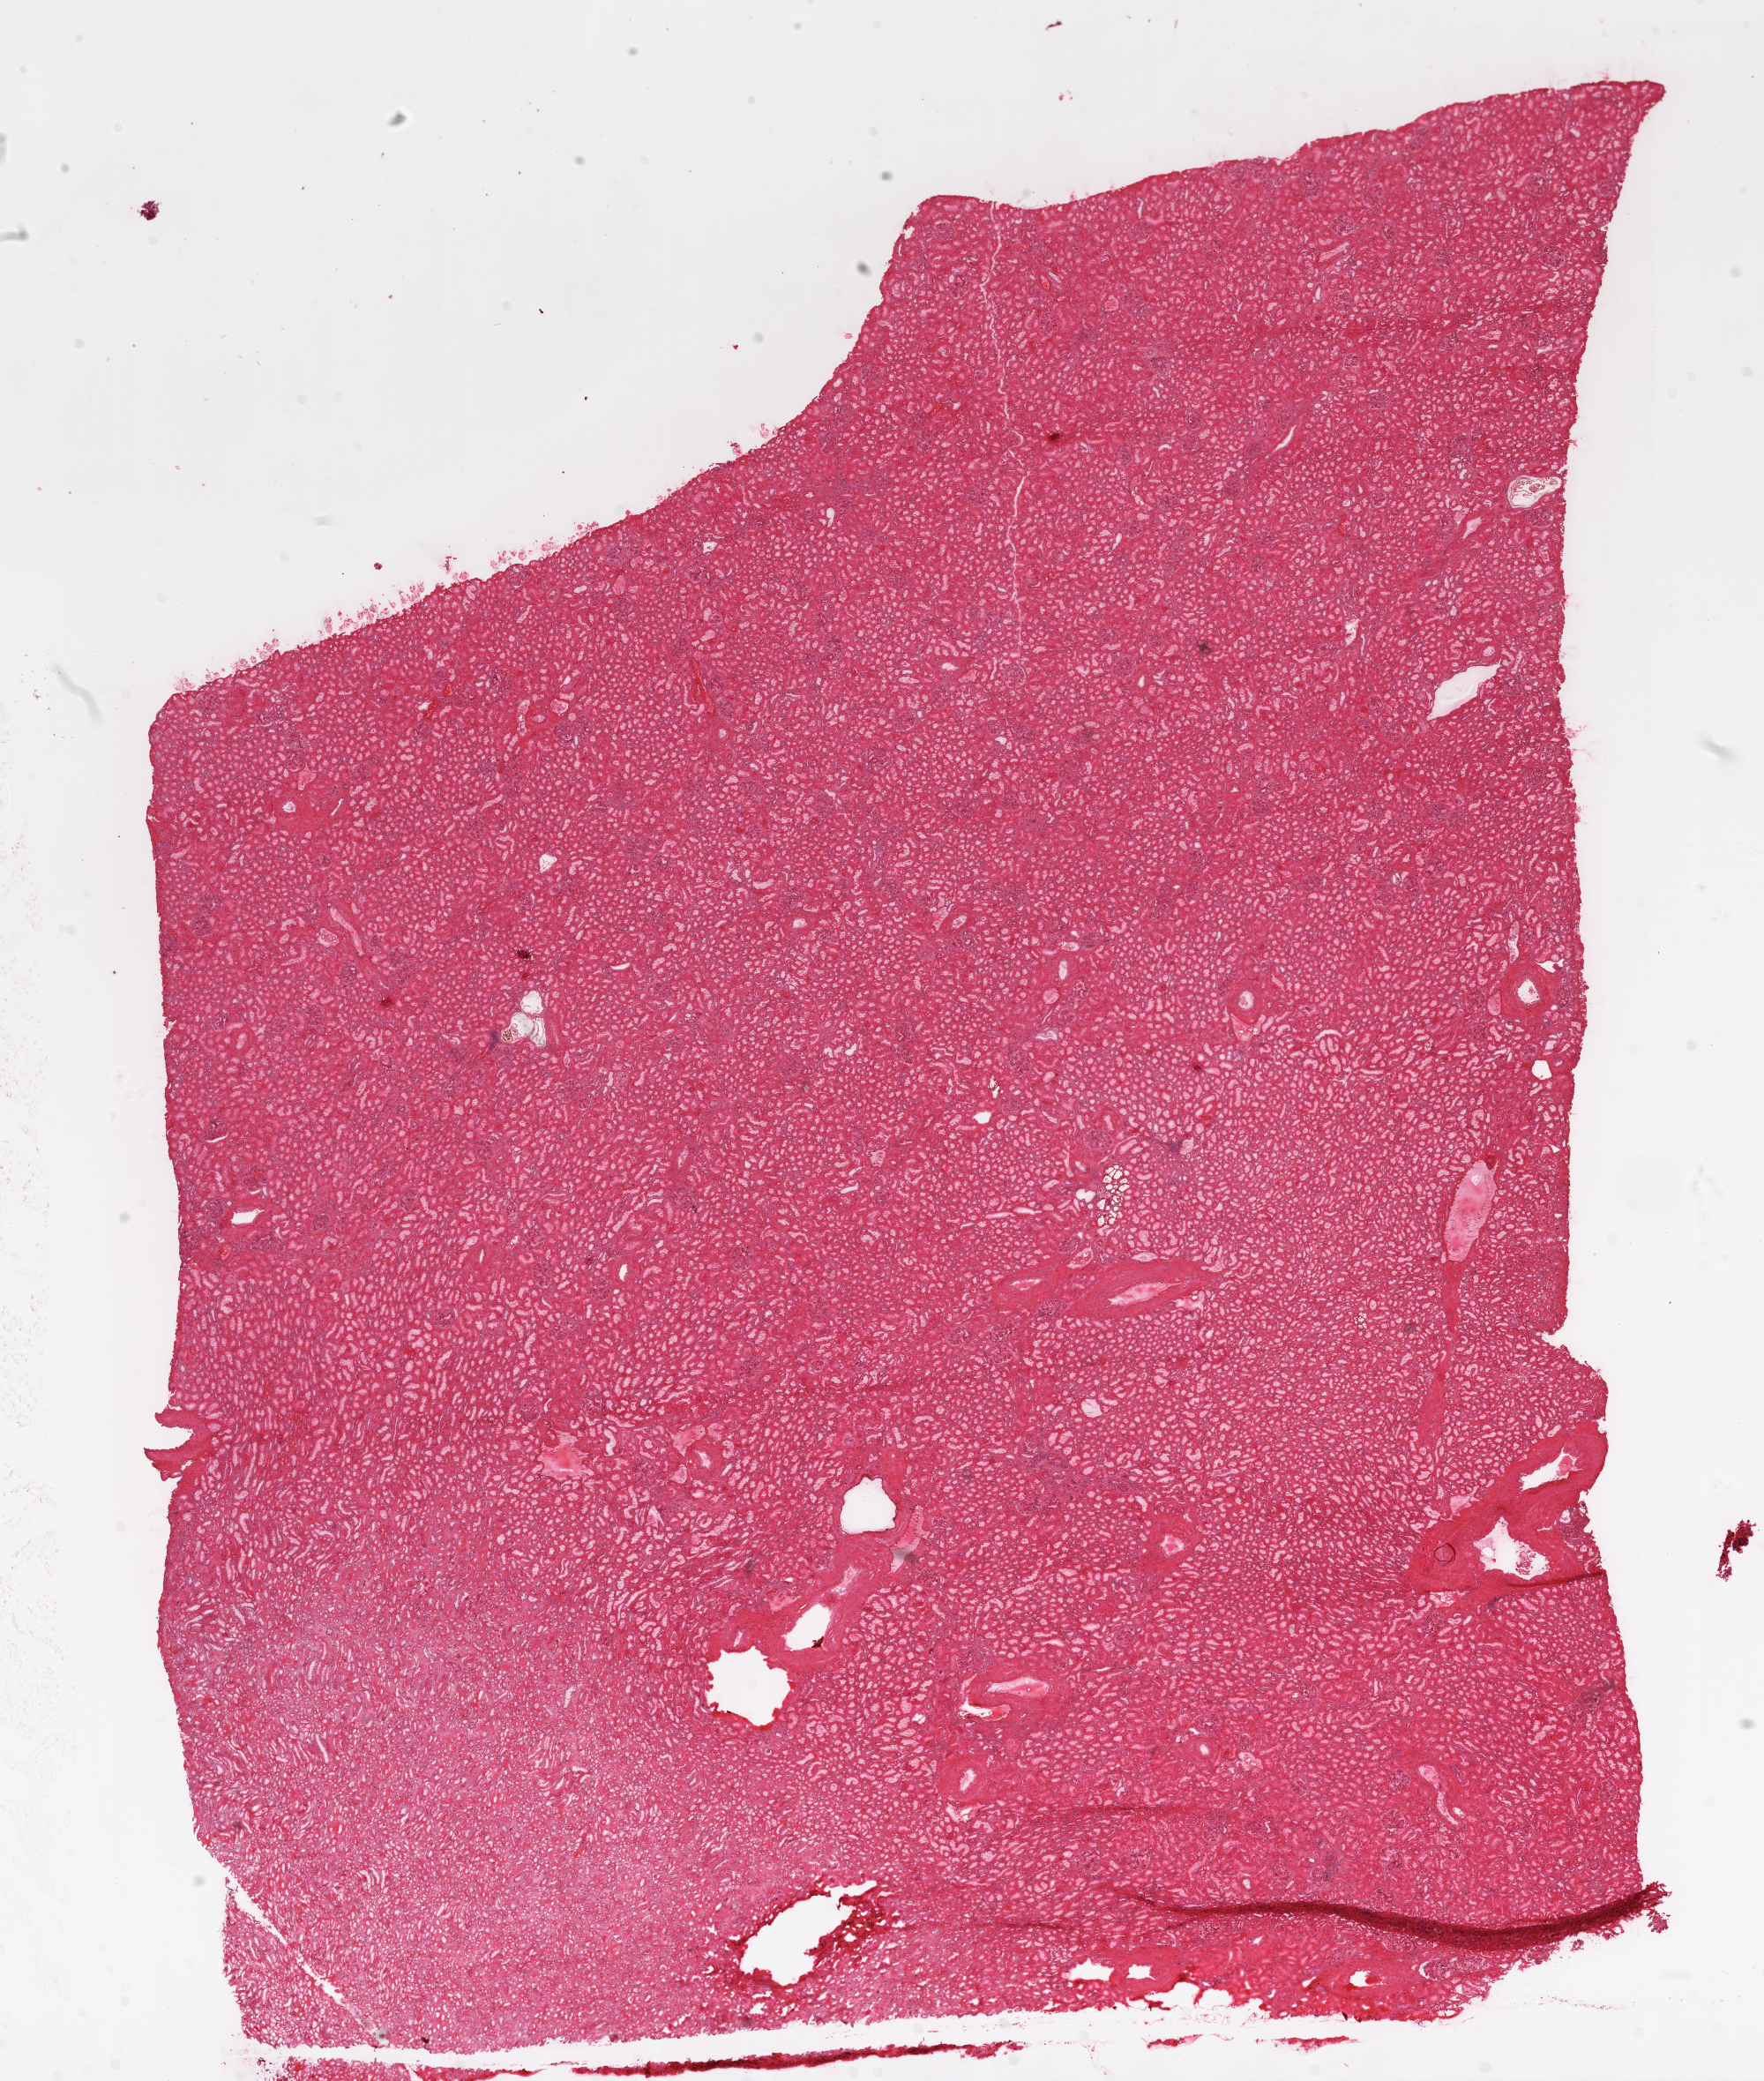
Digitized Hematoxylin and eosin (H&E) stained tissue section (whole slide) — low-resolution overview of the scanned area, about 16.0 x 18.9 mm (slide scanned at 20x), frozen section from the top of the tissue portion, kidney, solid tissue normal (non-tumour tissue) sample. Male patient; age at initial diagnosis 74 years.
This section: solid tissue normal (non-tumour) sample from the same patient. Patient diagnosis: Clear cell adenocarcinoma, NOS.